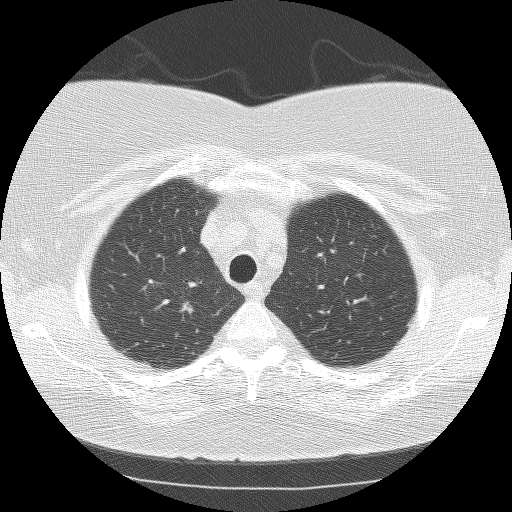
Chest CT (low-dose screening protocol), one axial image, baseline annual screen, lung window (W 1500 / L -600 HU), 2.5 mm slice thickness, lung (sharp) reconstruction kernel (BONE), slice 25 of 159 in the series, 512 × 512 image matrix. Female participant, aged 64 years at enrolment. Current smoker at enrolment.
Expert-annotated lung lesion, bounding box (x1, y1, x2, y2) in pixels: (170, 293, 211, 330). Reader record for this screening exam (exam-level; its link to the box is not recorded): non-calcified nodule or mass ≥4 mm, right upper lobe, 7 × 7 mm, smooth margins, soft tissue attenuation. Participant outcome: lung cancer diagnosed 314 days after this screen — small cell carcinoma, NOS, right hilum, stage IV (AJCC 6th edition).